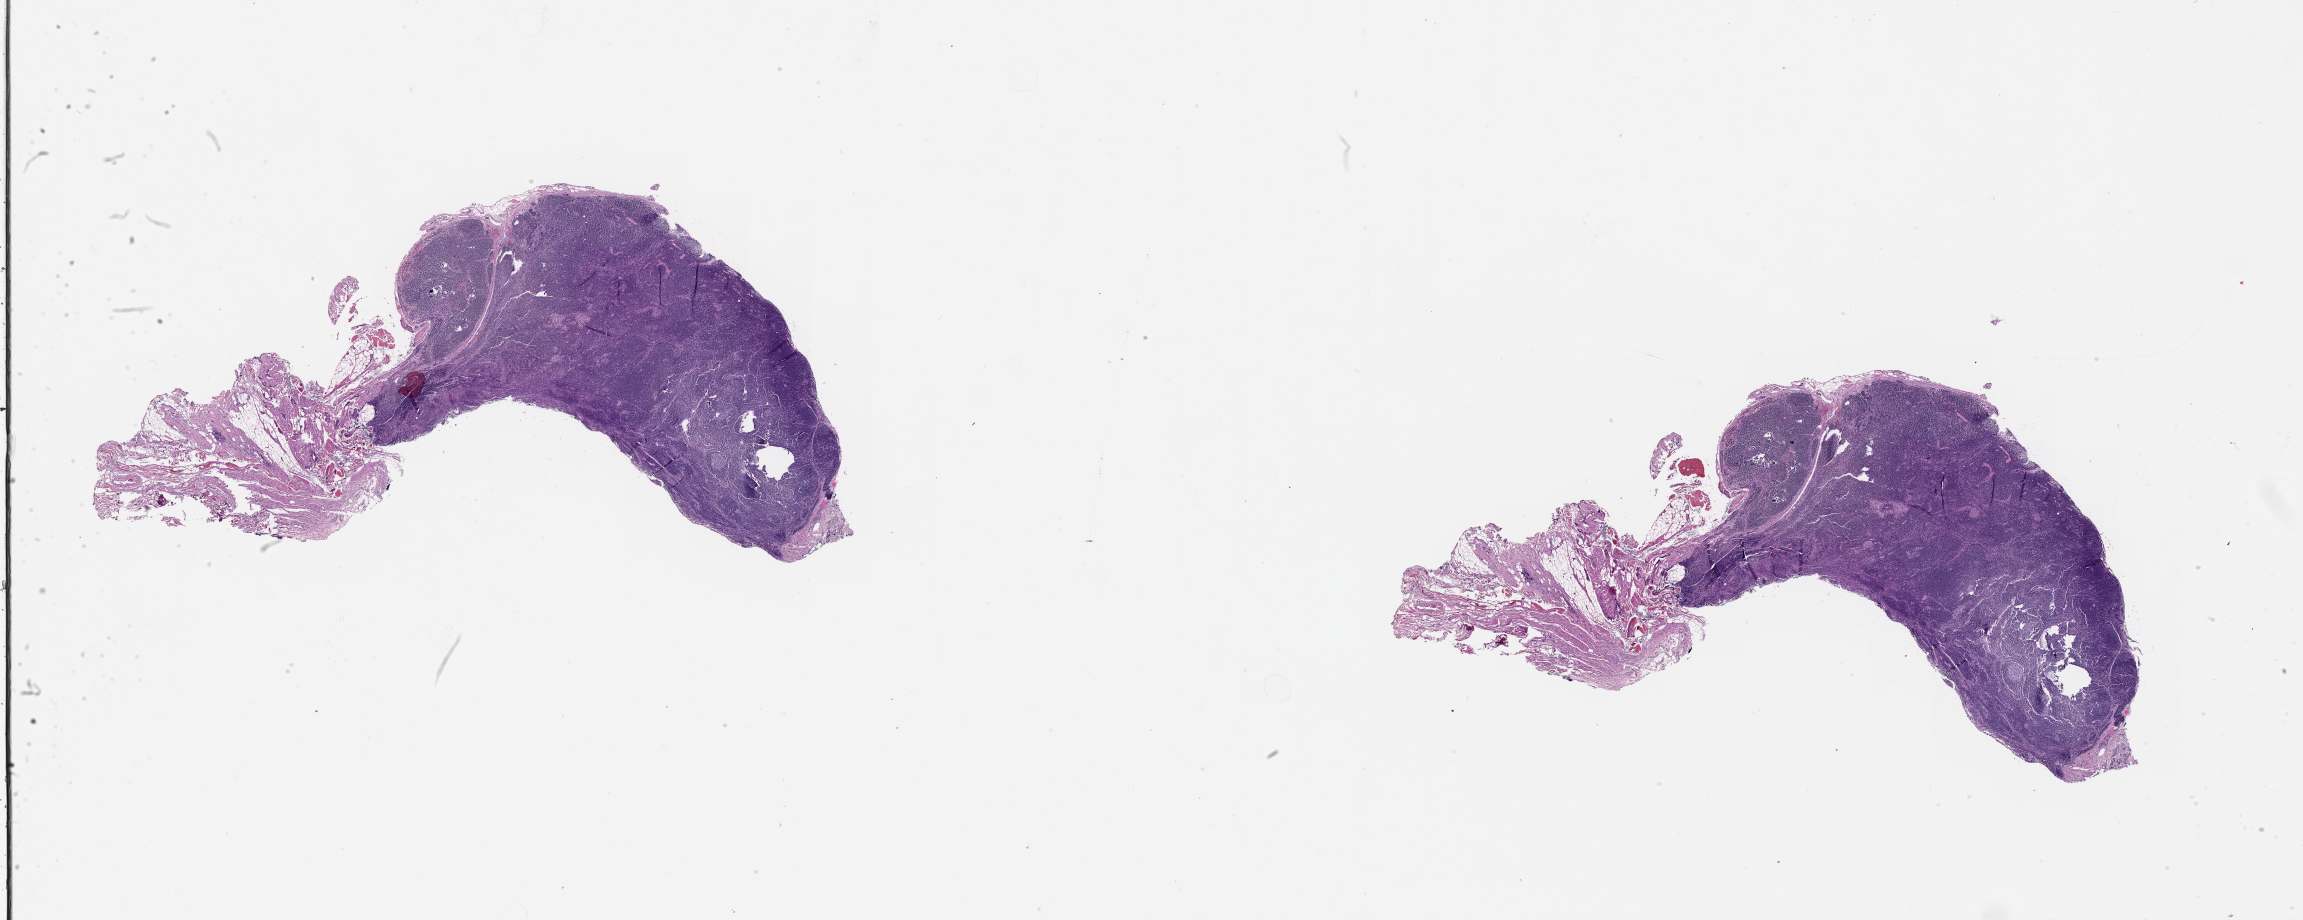
H&E whole-slide image — a low-resolution overview of the entire scanned area, about 37.1 x 14.8 mm. Normal (non-tumour) tissue sample, sampled site: pancreas. 69-year-old male patient.
This section: normal (non-tumour) tissue from the same patient. Patient diagnosis: Infiltrating duct carcinoma, NOS.